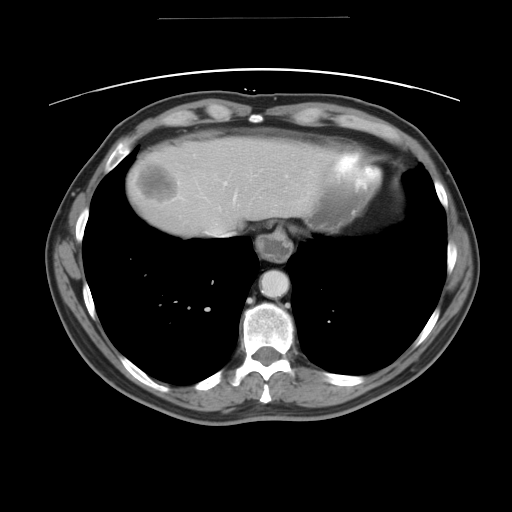
Contrast-enhanced abdominal CT, one axial slice. Position 42 of 49 along the scan axis. Reconstruction kernel STANDARD. 120 kVp. Intravenous contrast given. Soft-tissue window (W 400 / L 40 HU). 512 × 512 image matrix, field of view 413 × 413 mm. Male patient, age 57 years. Case-level facts recorded for this patient, not image findings: diagnosis: colorectal cancer liver metastases, imaged before liver resection.
Outlined on this slice (outlined manually by an expert reader):
- hepatic veins: bounding box (x1, y1, x2, y2) in pixels: (206, 195, 235, 235)
- liver: (125, 137, 336, 238)
- planned liver remnant (the part of the liver to remain after resection): (205, 137, 336, 238)
- liver metastasis: (135, 161, 180, 204)